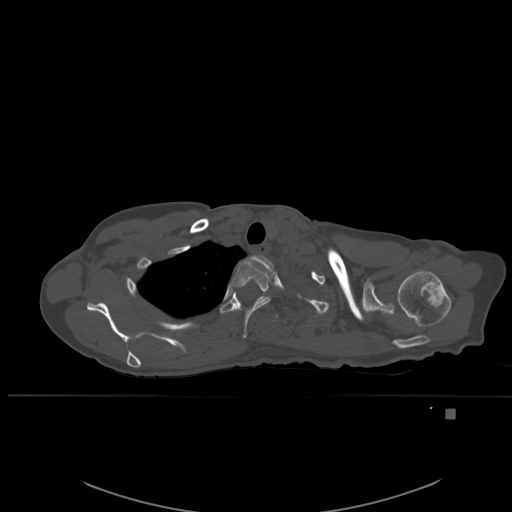
CT including the spine, one axial slice; position 432 of 537 along the scan axis; bone window (W 1800 / L 400 HU); 1.5 mm slice thickness; 512 × 512 image matrix, field of view 440 × 440 mm. Patient: female, 45 years. Case-level facts recorded for this patient, not image findings: primary cancer: lung.
Annotated regions visible in this slice (semi-automatic segmentation, software-assisted and operator-edited):
- T1 vertebra: bounding box (x1, y1, x2, y2) in pixels: (253, 256, 274, 272)
- T2 vertebra: (230, 259, 270, 338)
- T3 vertebra: (220, 291, 279, 319)